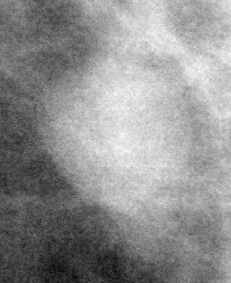
Crop from a digitized film mammogram around one marked abnormality, left breast, CC view, BI-RADS breast density category 2 (scale 1–4).
Marked abnormality: mass, shape oval, margins circumscribed; BI-RADS assessment category 3; subtlety rating 5 on a 1 (subtle) to 5 (obvious) scale; pathology result (as recorded, not read from the image): benign.